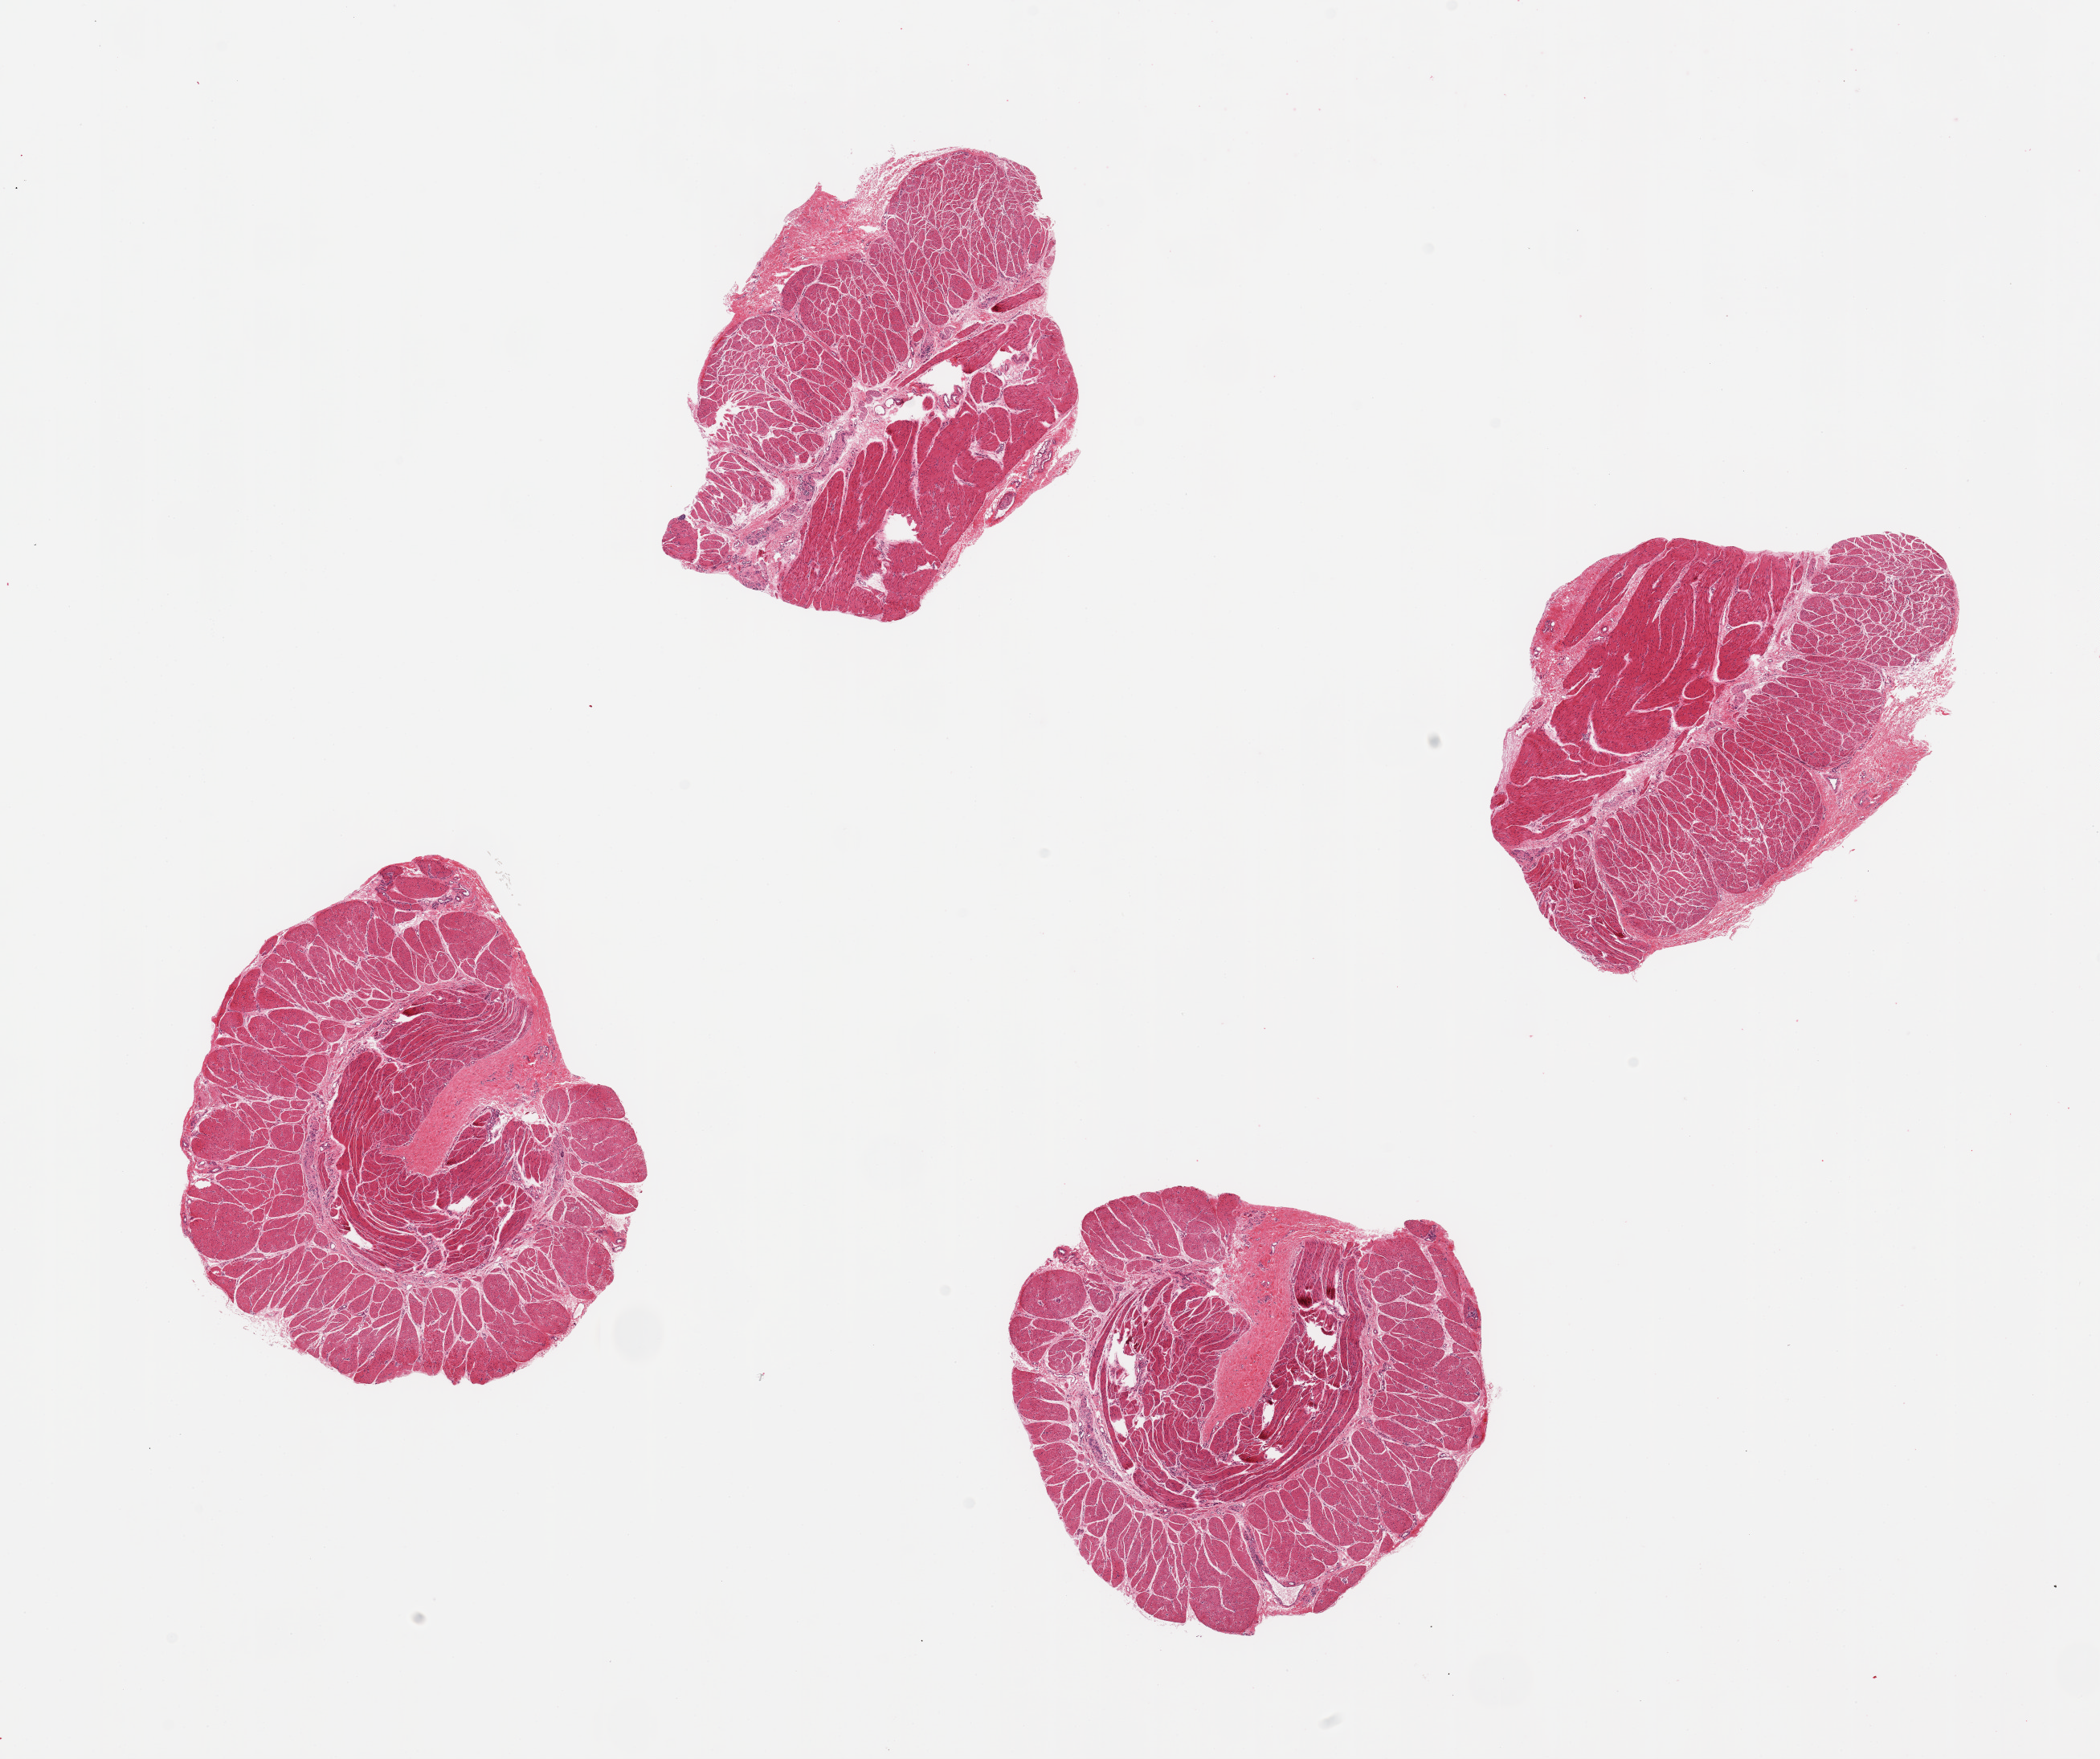
Whole-slide image, haematoxylin and eosin stain, a low-resolution overview of the entire scanned area, about 20.7 x 17.3 mm (from a 20x scan). PAXgene-fixed, paraffin-embedded tissue. Section of esophageal muscle (target tissue). Tissue donor sample.
• review note (as recorded): 4 pieces; well dissected